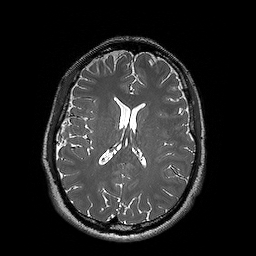
Brain MRI from a brain-tumour surgery series, one axial slice; slice 75 of 192 in the series (ordered by position); 256 × 256 image matrix. From the clinical record (not read from this slice): histopathology: Oligodendroglioma; WHO grade: 2; IDH mutation: yes; tumour location: Left Posterior Temporal.
Outlined on this slice (outlined manually by an expert reader):
- tumour: bounding box <163,168,179,181> (left, top, right, bottom; pixels)